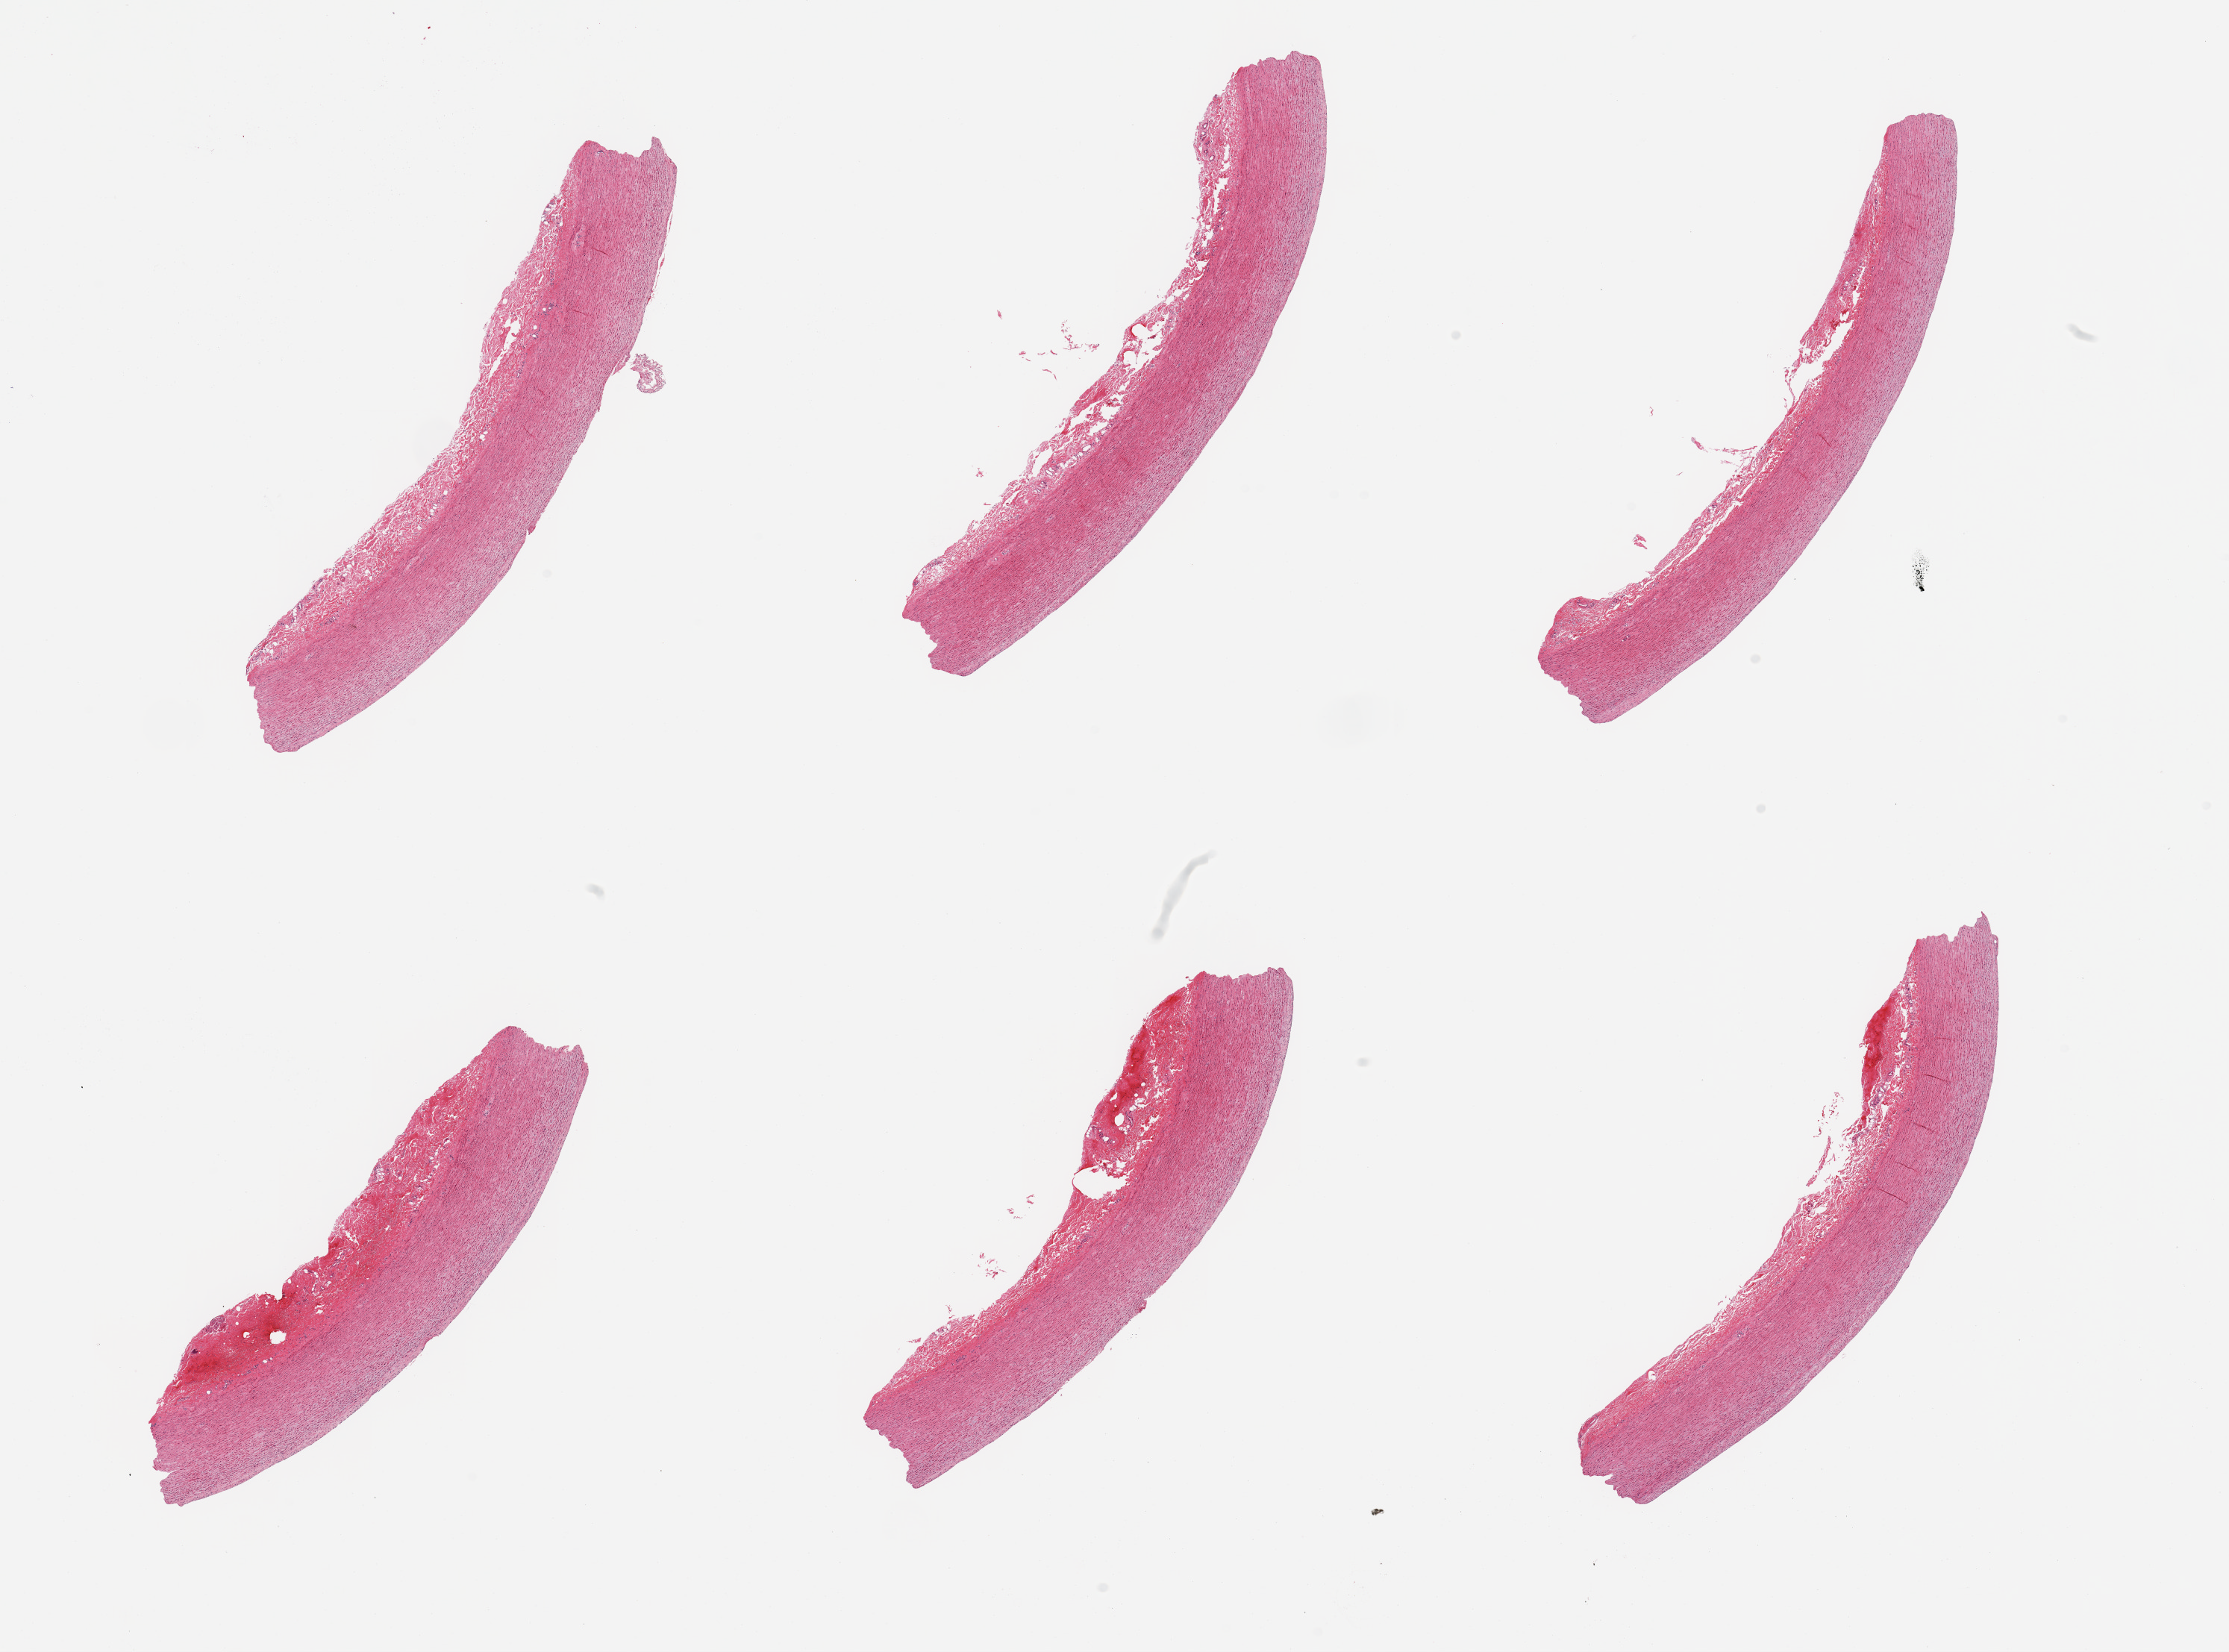
Digitized hematoxylin and eosin (H&E)-stained section — a low-resolution overview of the entire scanned area, about 23.6 x 17.5 mm. PAXgene-fixed, paraffin-embedded tissue. Section of aorta (target tissue). Tissue donor sample.
Review note (as recorded): 6 pieces; focal early atheromatous change.